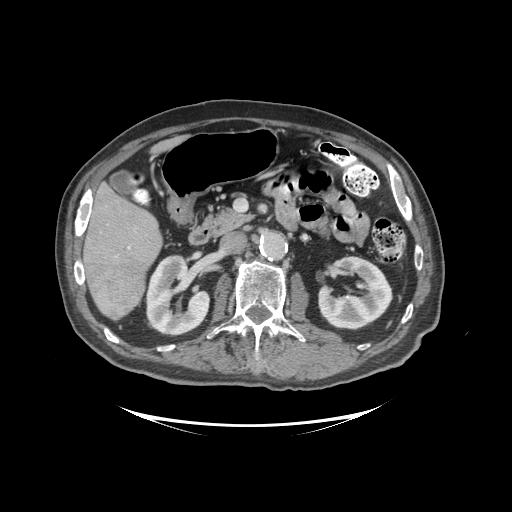
Contrast-enhanced abdominal CT (liver protocol), one axial slice. Position 44 of 99 along the scan axis. Soft-tissue window (W 400 / L 40 HU). 2.5 mm slice thickness. 512 × 512 image matrix, field of view 460 × 460 mm. Case-level facts recorded for this patient, not image findings: diagnosis: hepatocellular carcinoma (patient treated with transarterial chemoembolisation; whether this scan precedes or follows treatment is not stated here); TNM stage (as recorded): Stage-I; Child-Pugh class: A; tumour differentiation: moderately differentiated; tumour nodularity: uninodular.
Annotated regions visible in this slice (semi-automatically segmented with operator editing):
- liver parenchyma outside the tumour (the mass and vessels are separate outlines, so this box may not span the whole liver): bounding box (x1, y1, x2, y2) in pixels: (82, 149, 162, 320)
- mass: (86, 257, 145, 316)
- liver vessels: (86, 205, 130, 249)